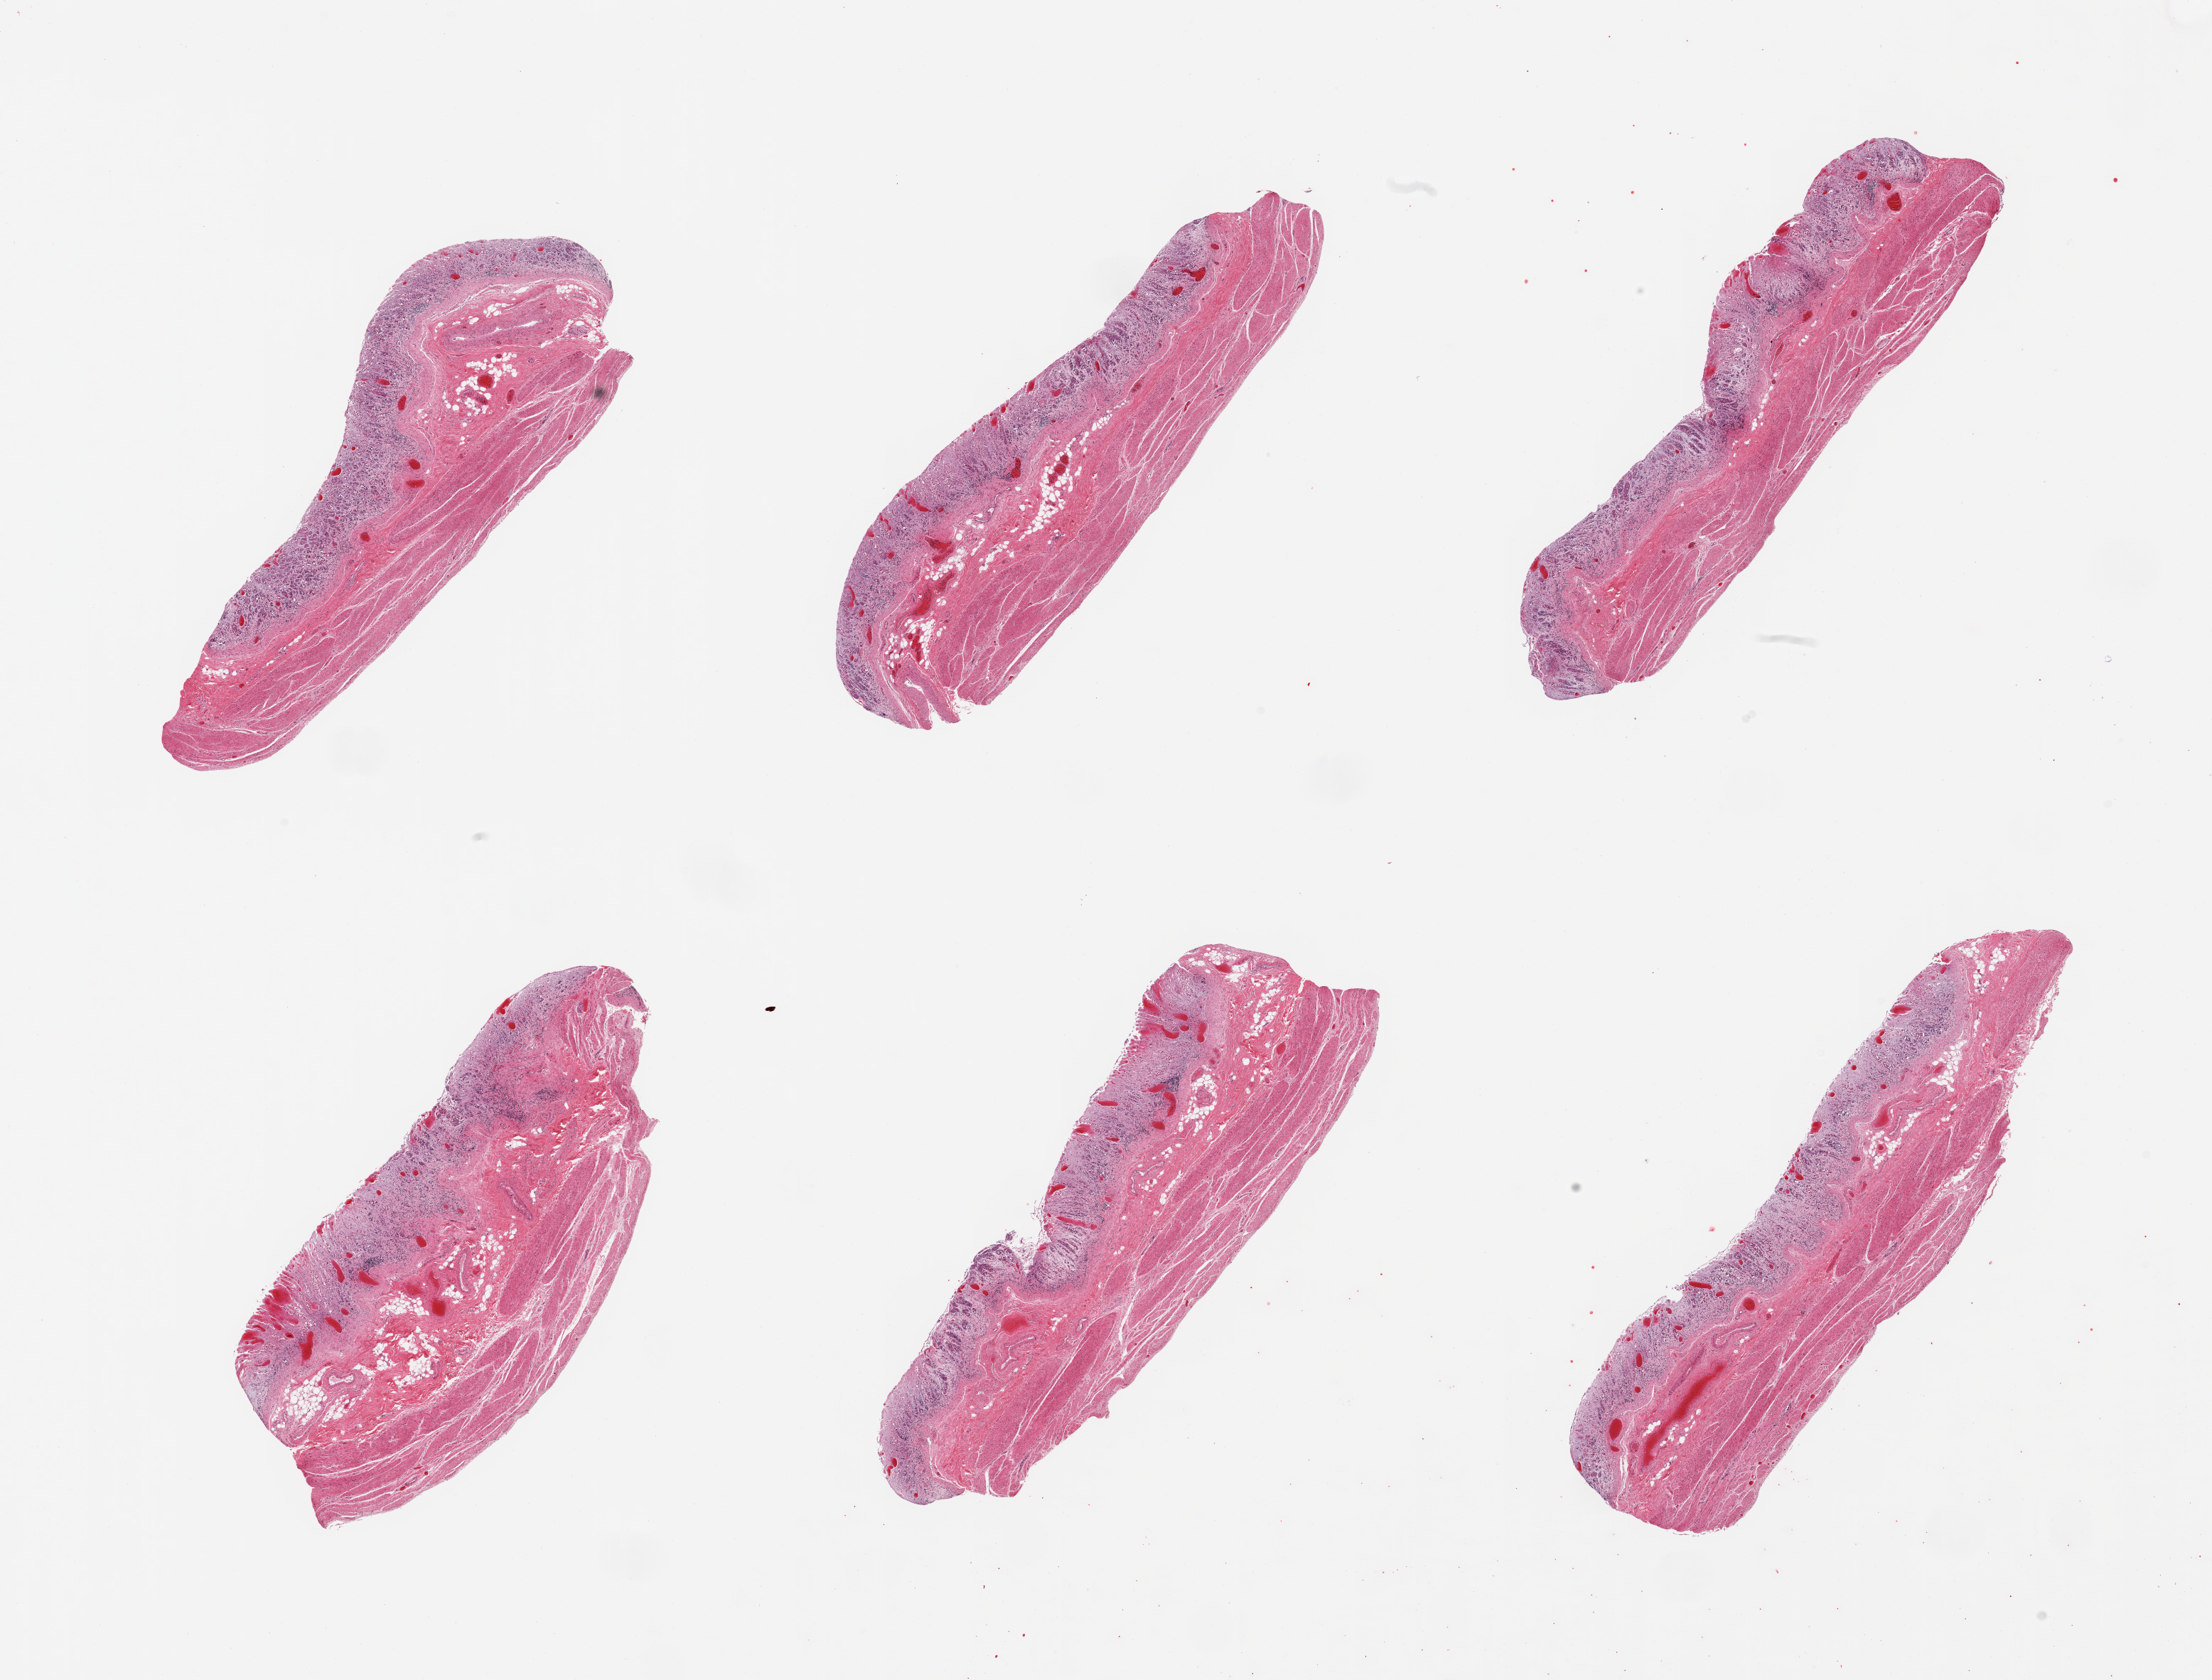
Digitized H&E-stained section — a low-resolution overview of the entire scanned area, about 24.6 x 18.7 mm; PAXgene-fixed, paraffin-embedded tissue; section of stomach (target tissue); donor tissue sample. Male donor.
- pathologist's review note for this sample: 6 pieces; mucosa severely autolyzed, muscularis moderately